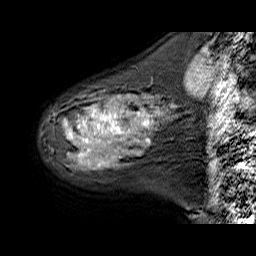
Breast MRI (dynamic contrast-enhanced), one sagittal slice; slice 17 of 60 in the series (ordered by position); dynamic contrast-enhanced series, time point 2 of 6 at this slice position (early post-contrast); 1.5 T; TE 6.3 ms, TR 32.9 ms; 4 mm slice thickness; 256 × 256 image matrix, field of view 200 × 200 mm. Female patient. Case-level facts recorded for this patient, not image findings: setting: breast cancer imaged before/during neoadjuvant chemotherapy; receptor status: HER2-positive.
Outlined on this slice (semi-automatic segmentation, software-assisted and operator-edited):
- analysis volume of interest (the breast-tissue region the enhancement analysis was run in; not a lesion): bounding box (x1, y1, x2, y2) in pixels: (52, 78, 175, 171)
- tumour enhancement mask (voxels above the 100 % enhancement threshold inside the analysis volume of interest): (70, 114, 150, 167)